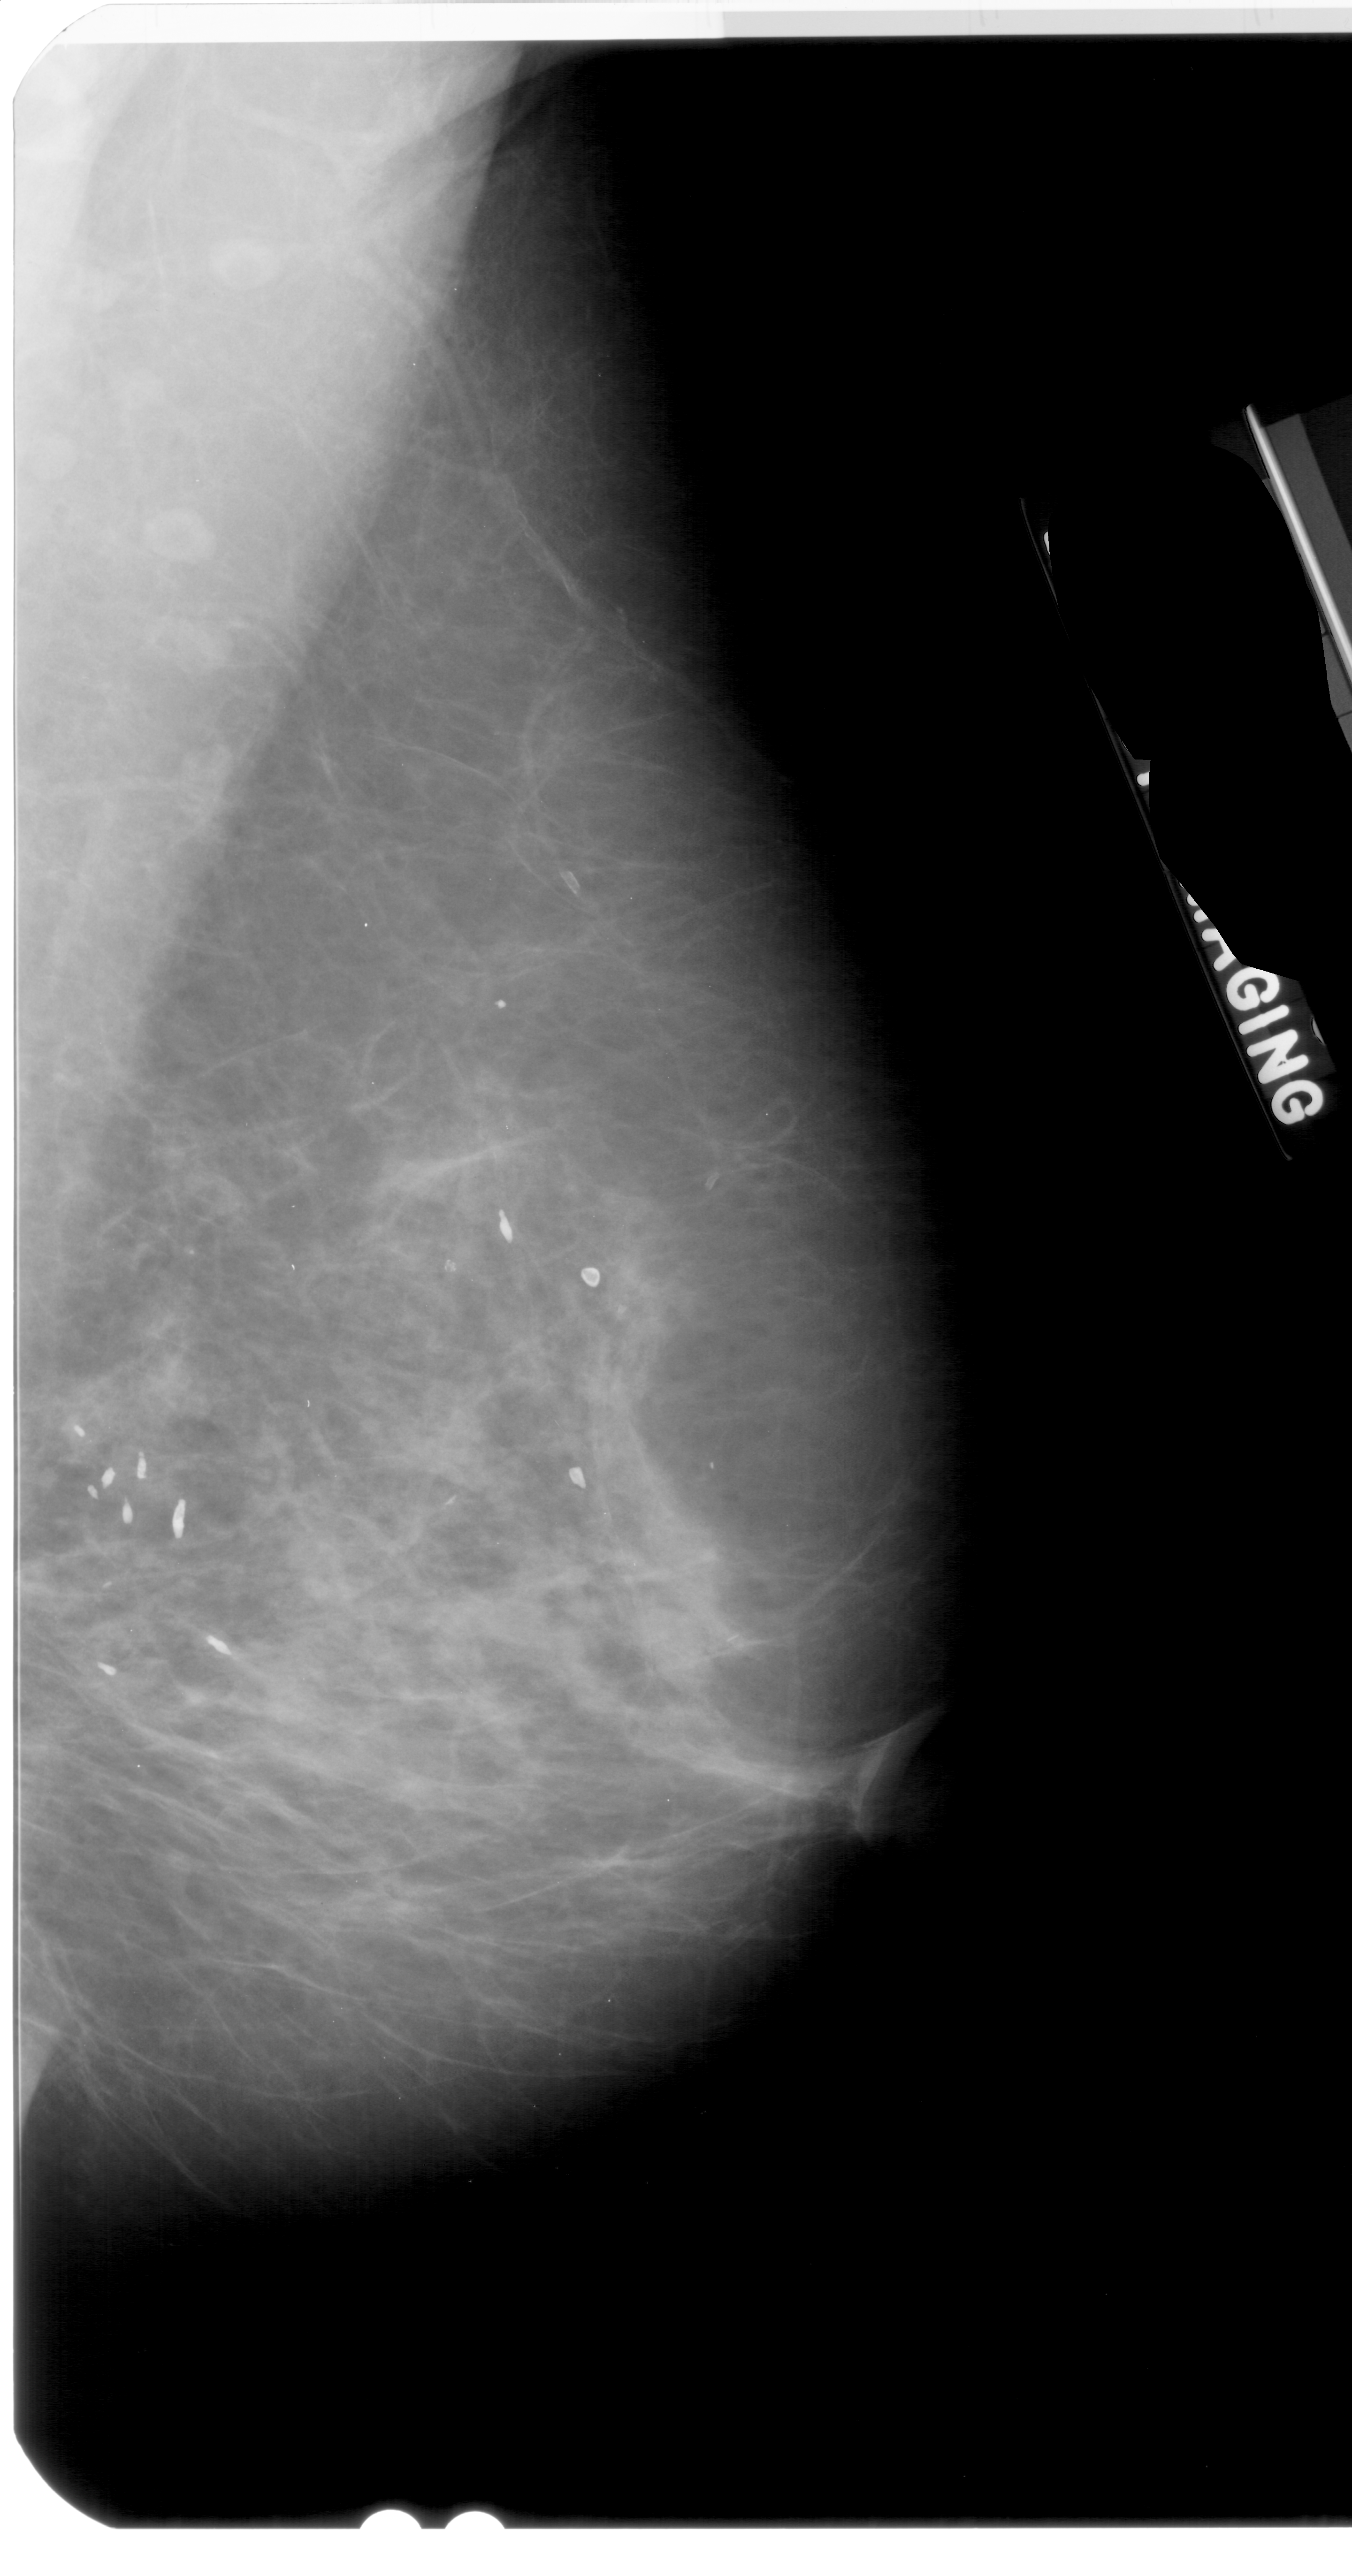
Digitized screen-film mammogram, right breast, mediolateral oblique (MLO) view, BI-RADS breast density category 2 (scale 1–4).
- Finding: mass, shape lobulated, margins ill defined; BI-RADS assessment category 4; subtlety rating 1 on a 1 (subtle) to 5 (obvious) scale; pathology result (as recorded, not read from the image): benign.